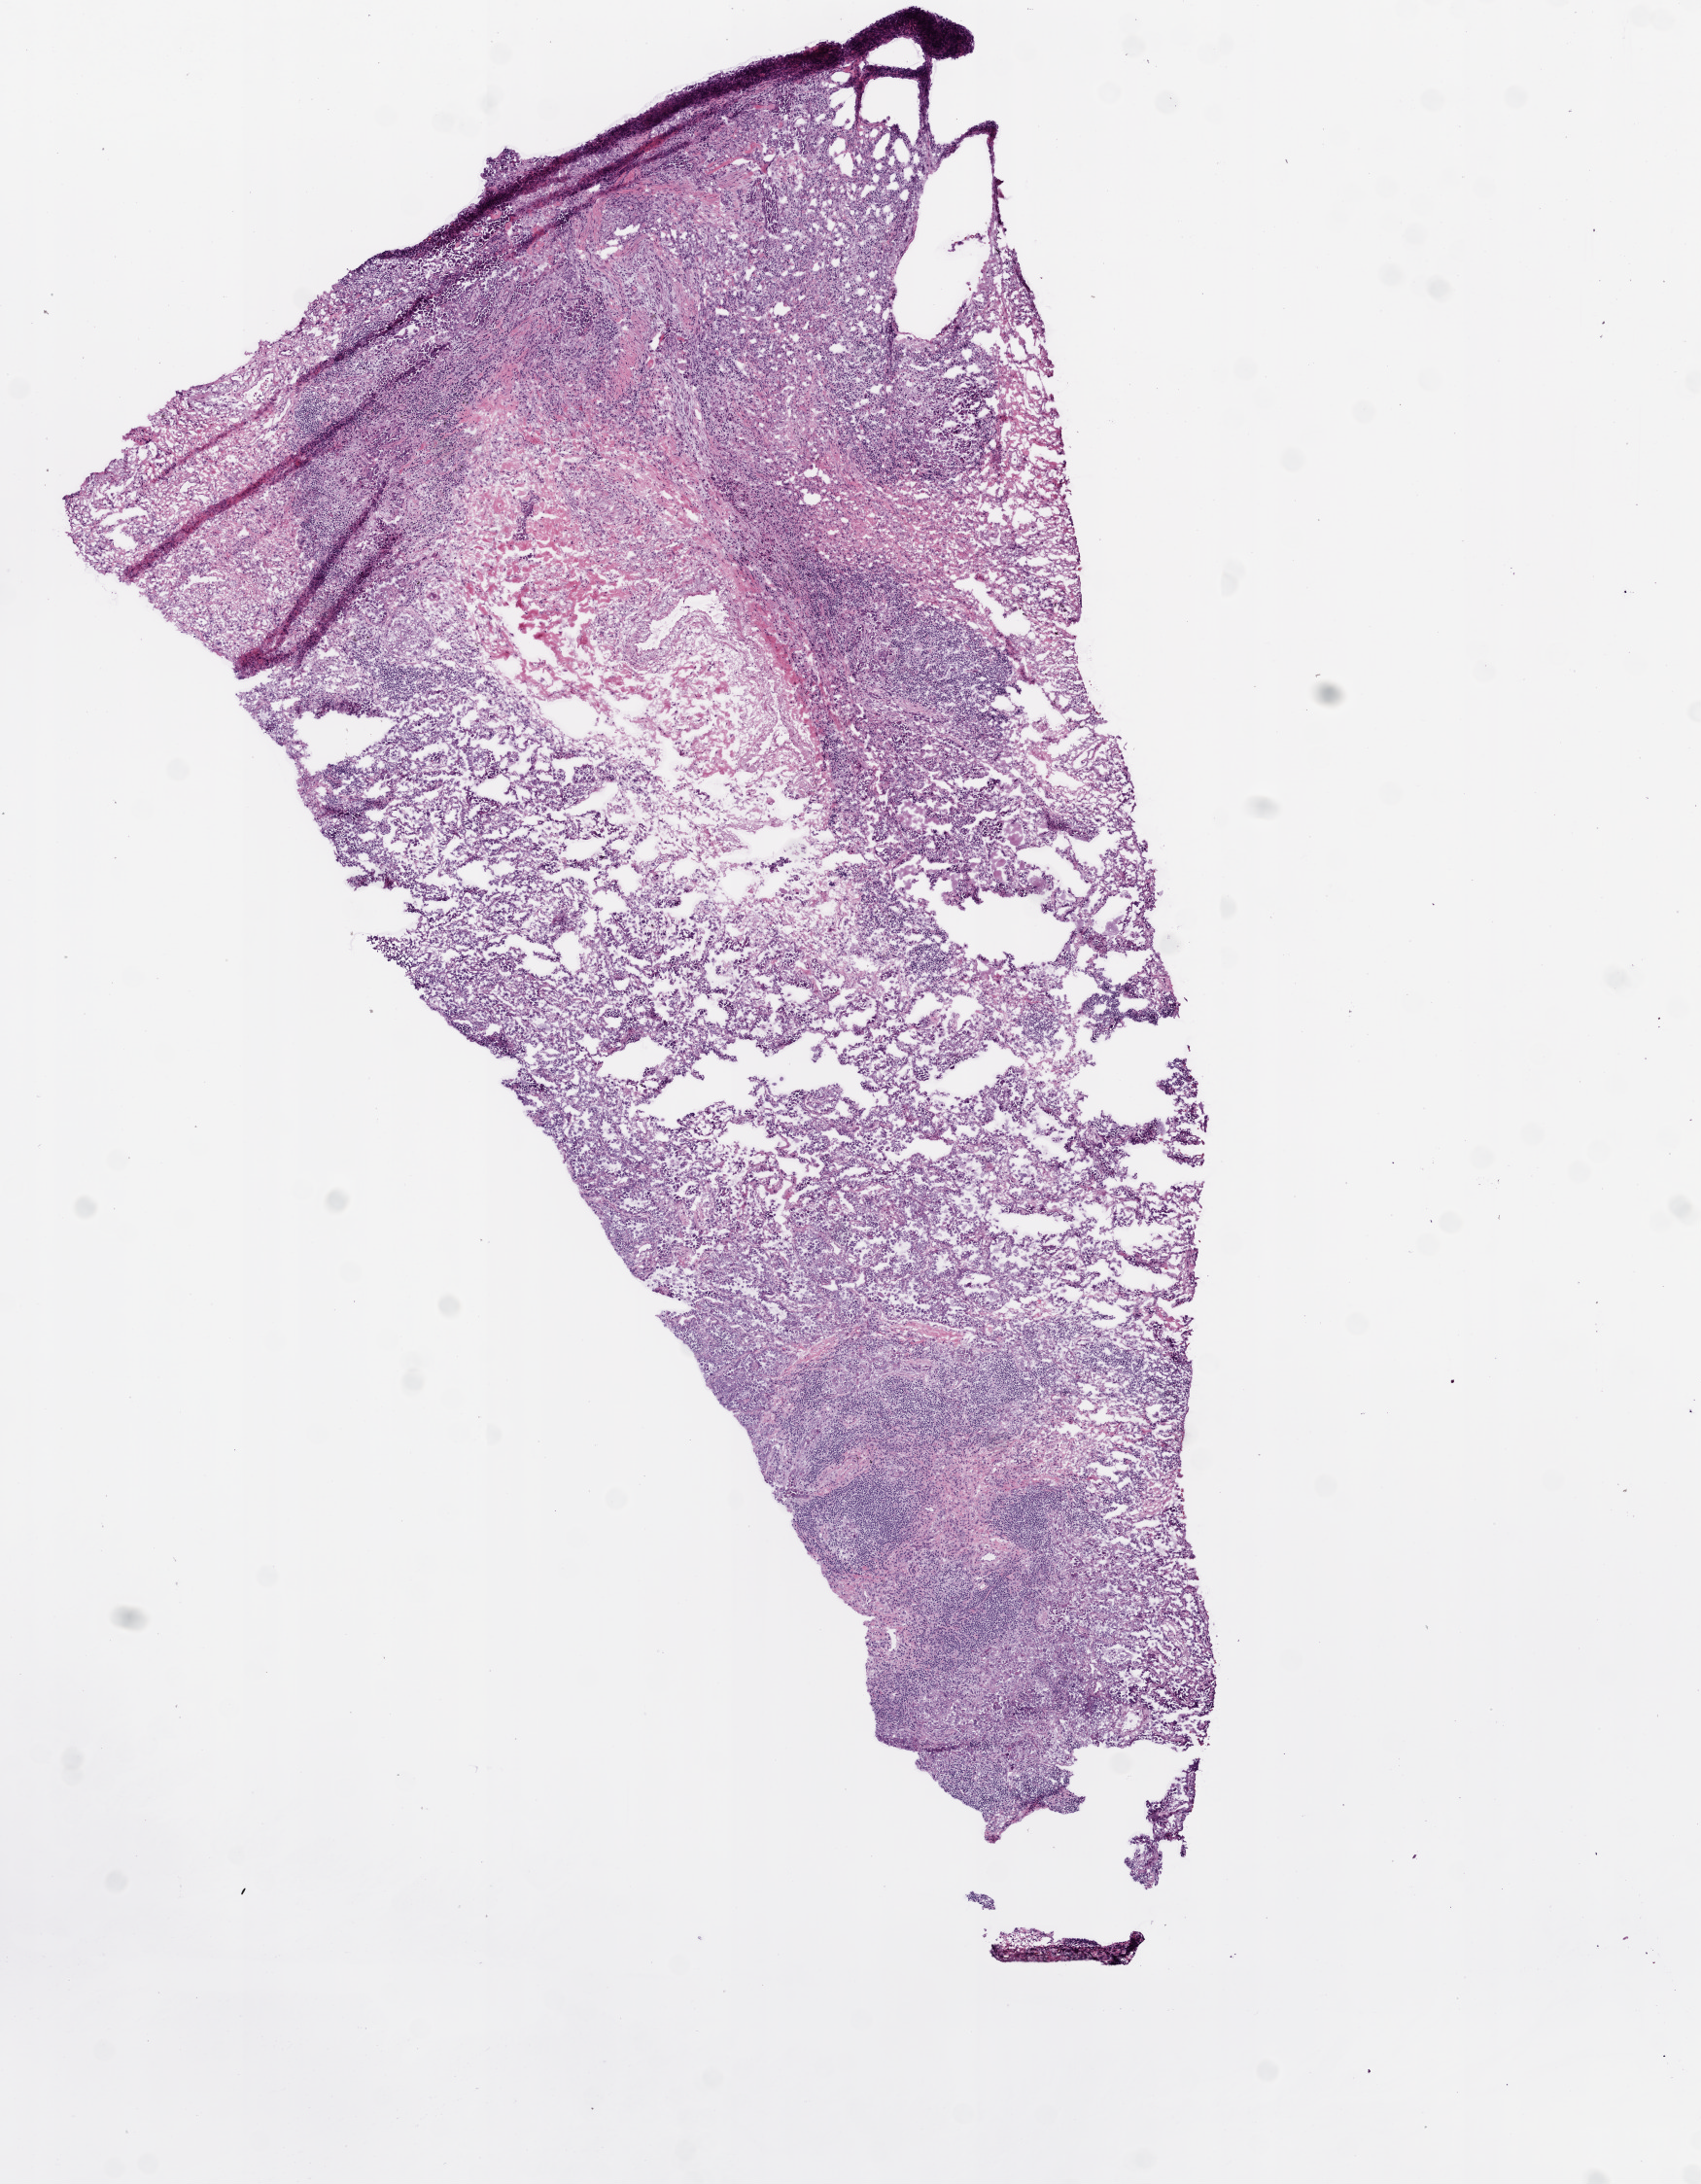
Whole-slide histology image, Hematoxylin and eosin (H&E) stained, a low-resolution overview of the entire scanned area, about 7.0 x 9.0 mm; frozen section from the bottom of the tissue portion; lung, primary tumour sample. Female, age 65 years at initial diagnosis. Pathologist review of this section (percent, as recorded): tumour cells 70%, tumour nuclei 80%, normal cells 0%, stromal cells 20%, necrosis 10%. Infiltration values recorded for this section: lymphocyte infiltration 20%.
AJCC pathologic stage: IA (6th edition). Diagnosis: Adenocarcinoma, NOS (upper lobe, lung). Laterality: left.